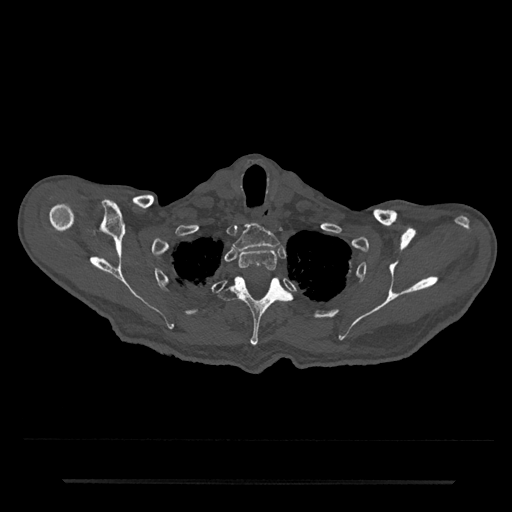
CT including the spine, one axial slice. 120 kVp. Bone window (W 1800 / L 400 HU). 512 × 512 image matrix. Patient: male, 74 years. From the clinical record (not read from this slice): primary cancer: prostate.
Structures marked on this image (semi-automatically segmented with operator editing):
- T1 vertebra: bounding box (x1, y1, x2, y2) in pixels: (232, 224, 279, 251)
- T2 vertebra: (239, 249, 278, 272)
- T3 vertebra: (219, 277, 292, 346)